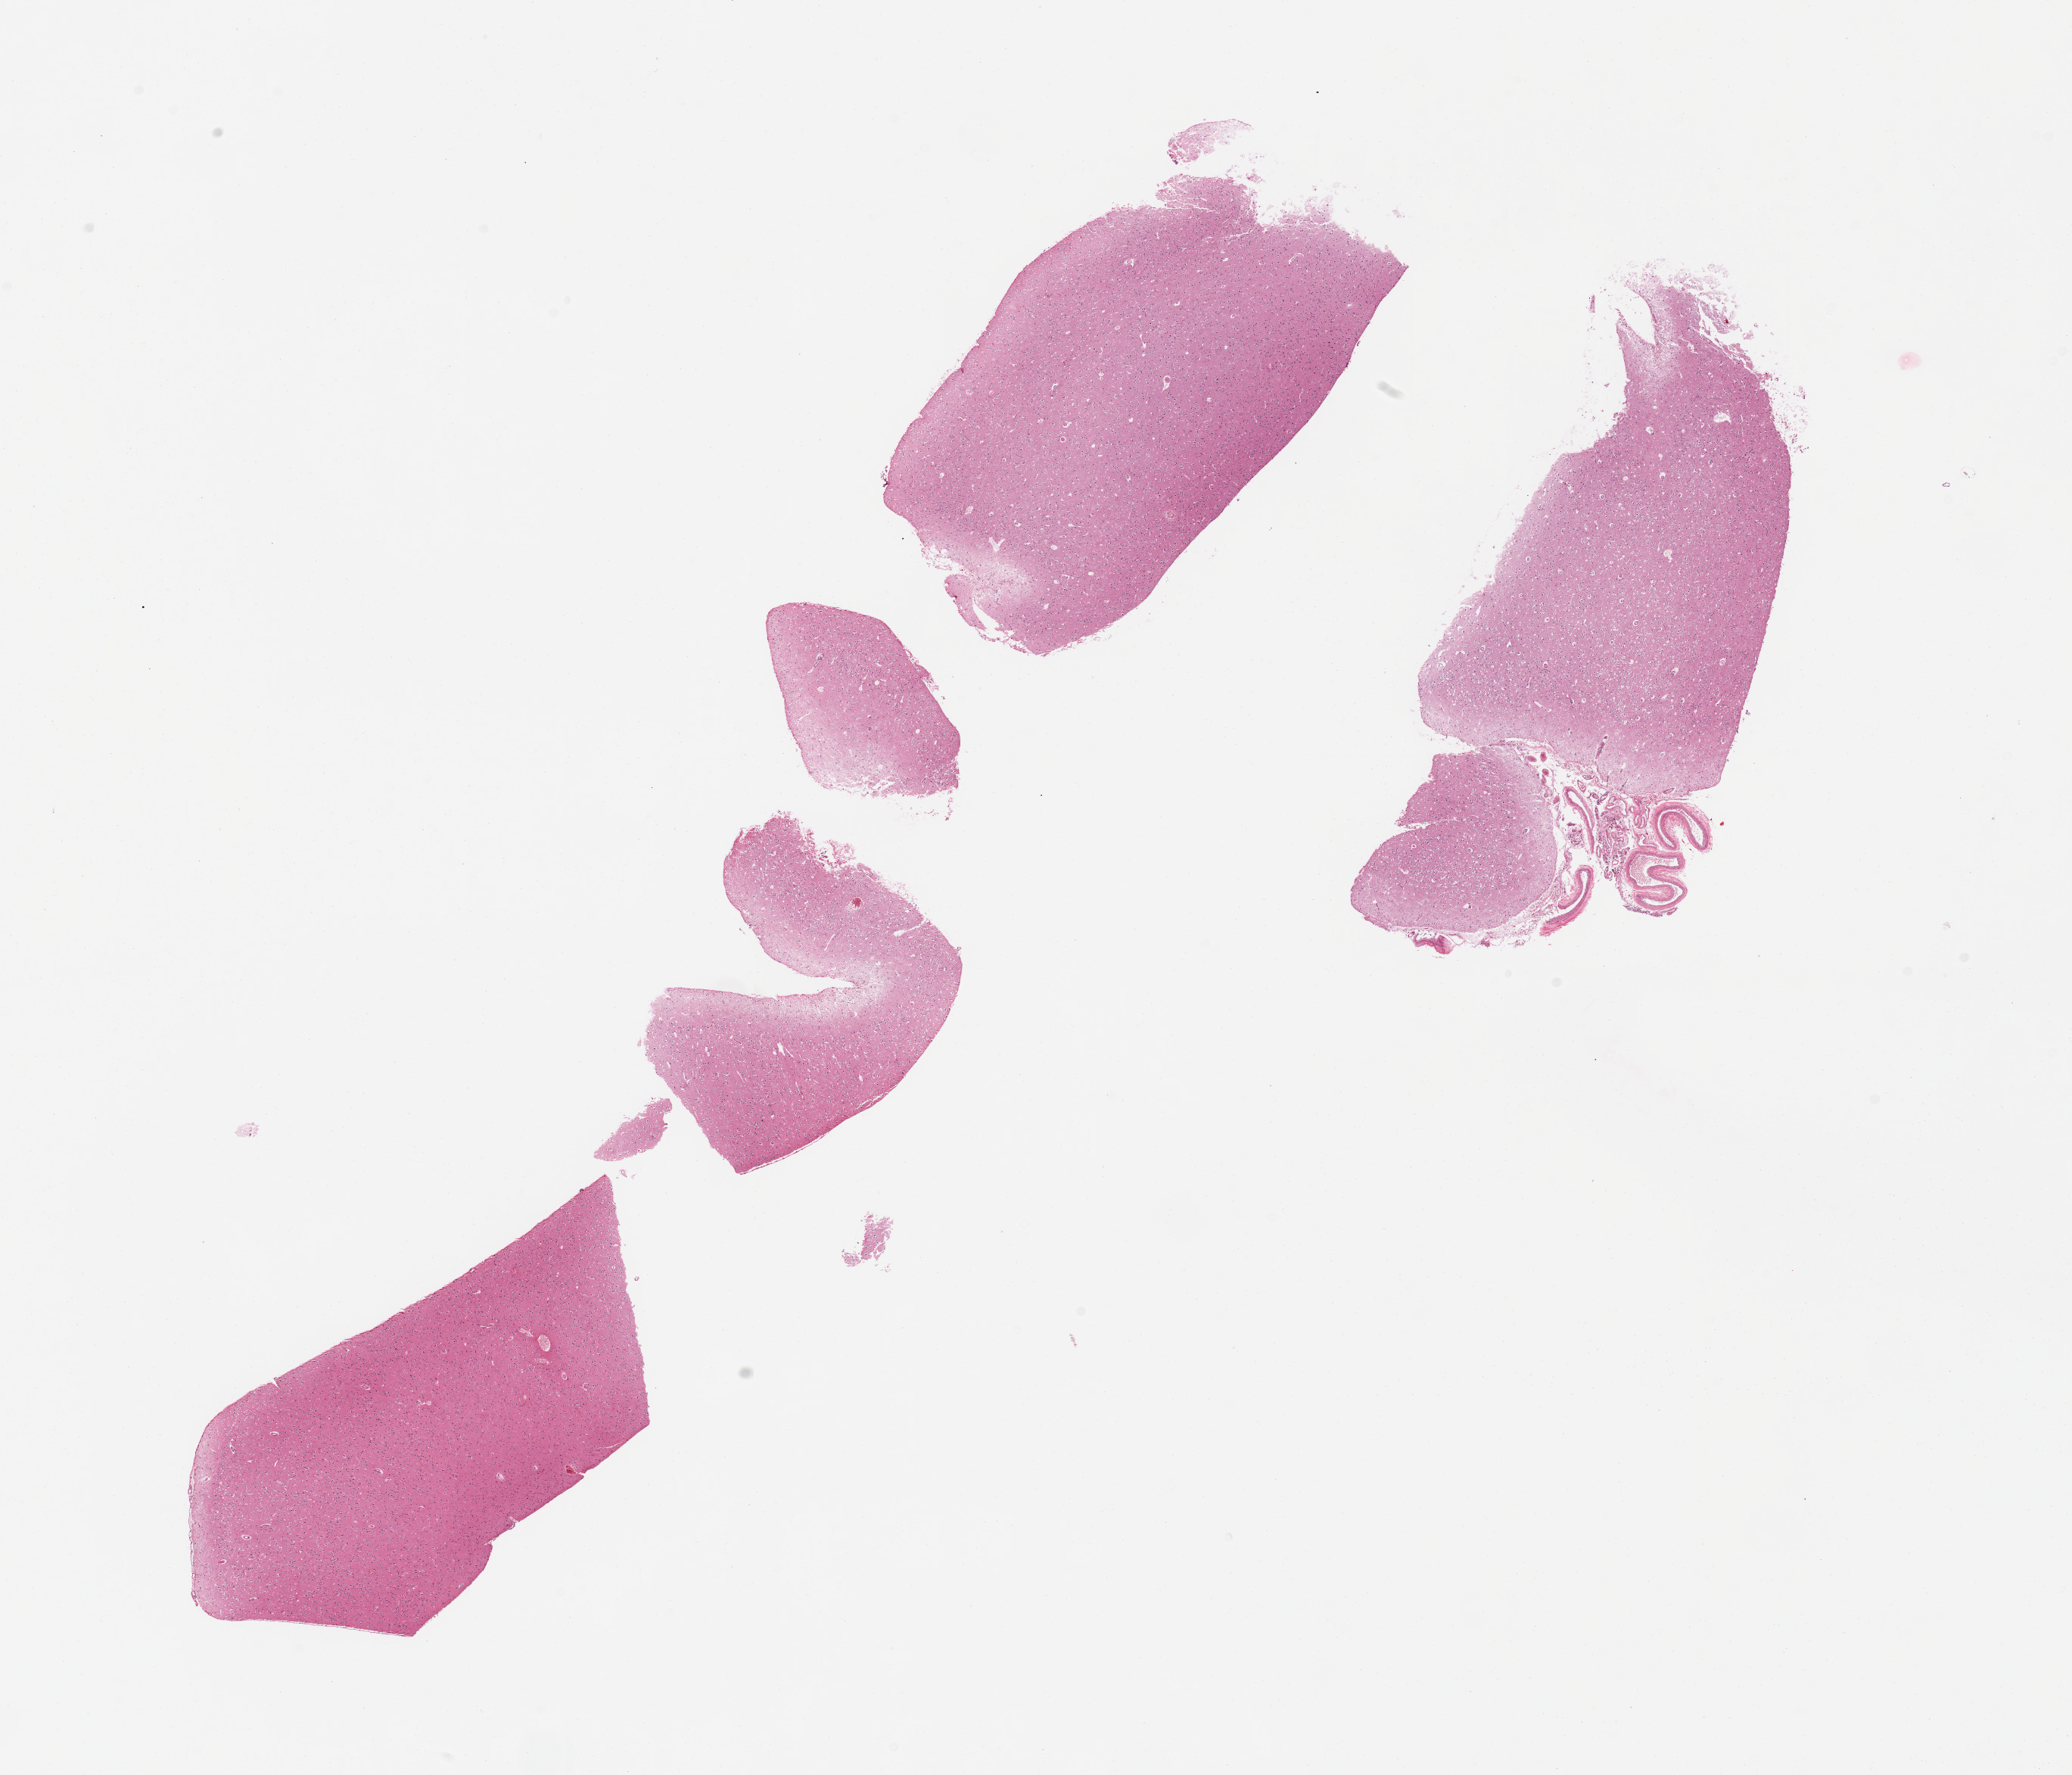
H&E whole-slide image — a low-resolution overview of the entire scanned area, about 21.7 x 18.5 mm. PAXgene-fixed, paraffin-embedded tissue. Sampled site (target tissue): cerebral cortex. Donor tissue sample.
Pathologist's review note for this sample: 4 pieces, some fragmentation; 1 piece has adherent meninges.